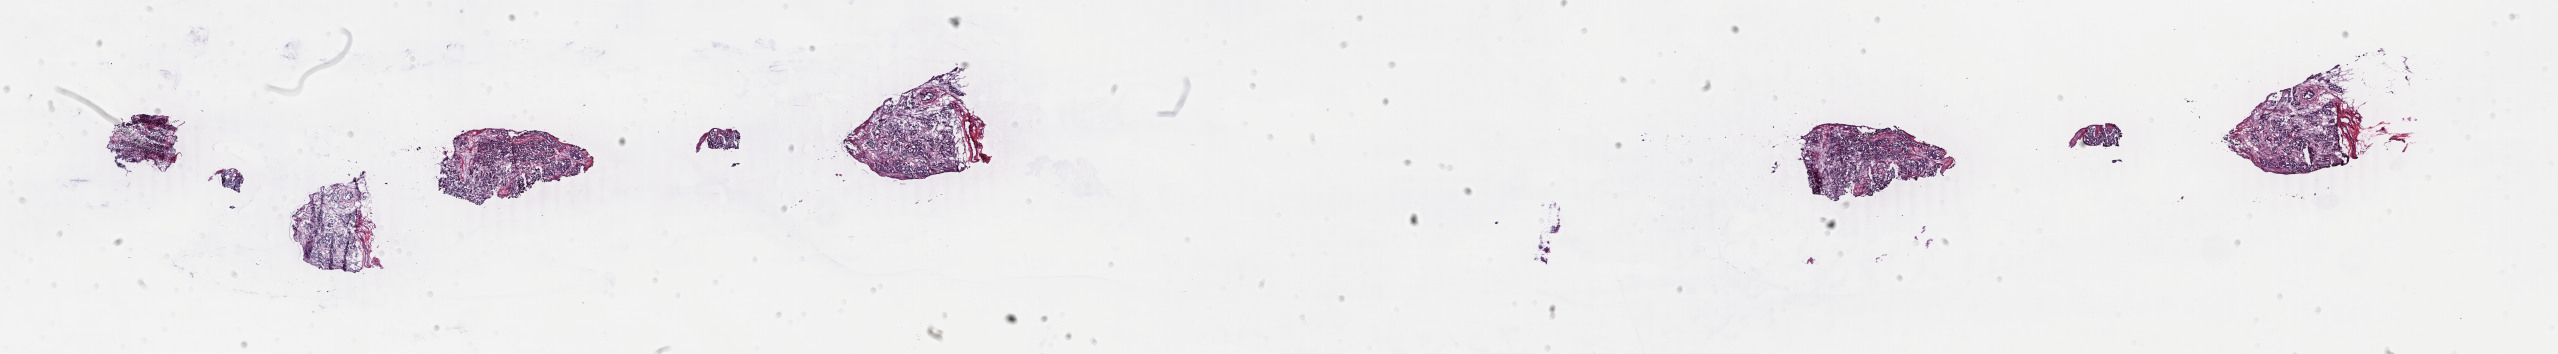
Digitized Hematoxylin and eosin (H&E) stained tissue section (whole slide), whole scanned area (about 40.7 x 5.6 mm, slide scanned at 40x) shown as a low-resolution overview. Frozen section from the bottom of the tissue portion. Breast, primary tumour sample. Female, age 73 years at initial diagnosis. Slide review estimates, as recorded: tumour cells 50%, tumour nuclei 85%, normal cells 5%, stromal cells 43%, necrosis 2%. Infiltration values recorded for this section: lymphocyte infiltration 3%, monocyte infiltration 2%, neutrophil infiltration 0%.
Histologic diagnosis: Infiltrating duct carcinoma, NOS. AJCC pathologic stage: IA (5th edition). Lymph nodes positive (case pathology): 0 of 1 examined.